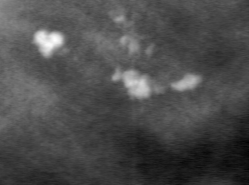
Region of interest cut from a scanned film mammogram (one marked finding), right breast, MLO view, BI-RADS breast density category 3 (scale 1–4).
- Finding: calcifications, morphology dystrophic, distribution clustered; BI-RADS assessment category 3; pathology (as recorded): benign.